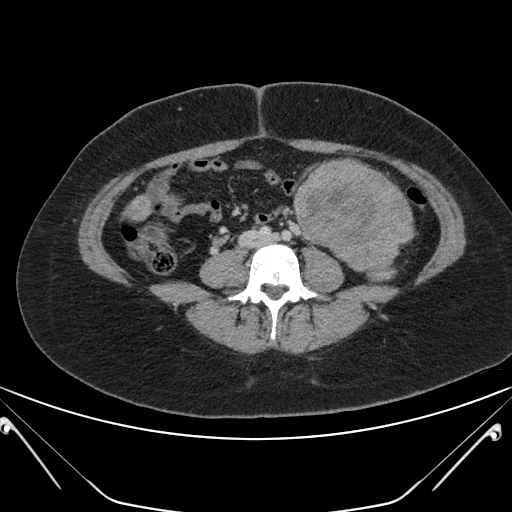
Contrast-enhanced abdominal CT, one axial slice. Position 79 of 168 along the scan axis. 120 kVp. Intravenous contrast given. Soft-tissue window (W 400 / L 40 HU). 512 × 512 image matrix, field of view 394 × 394 mm. Female patient, age 26 years. Case-level facts recorded for this patient, not image findings: diagnosis: adrenocortical carcinoma; tumour side: left adrenal; tumour size at pathology: 28 cm; Ki-67 index: 20 %; stage (as recorded): 2.
Annotated regions visible in this slice (semi-automatic segmentation, software-assisted and operator-edited):
- mass: box from (x=297, y=162) to (x=412, y=279) px